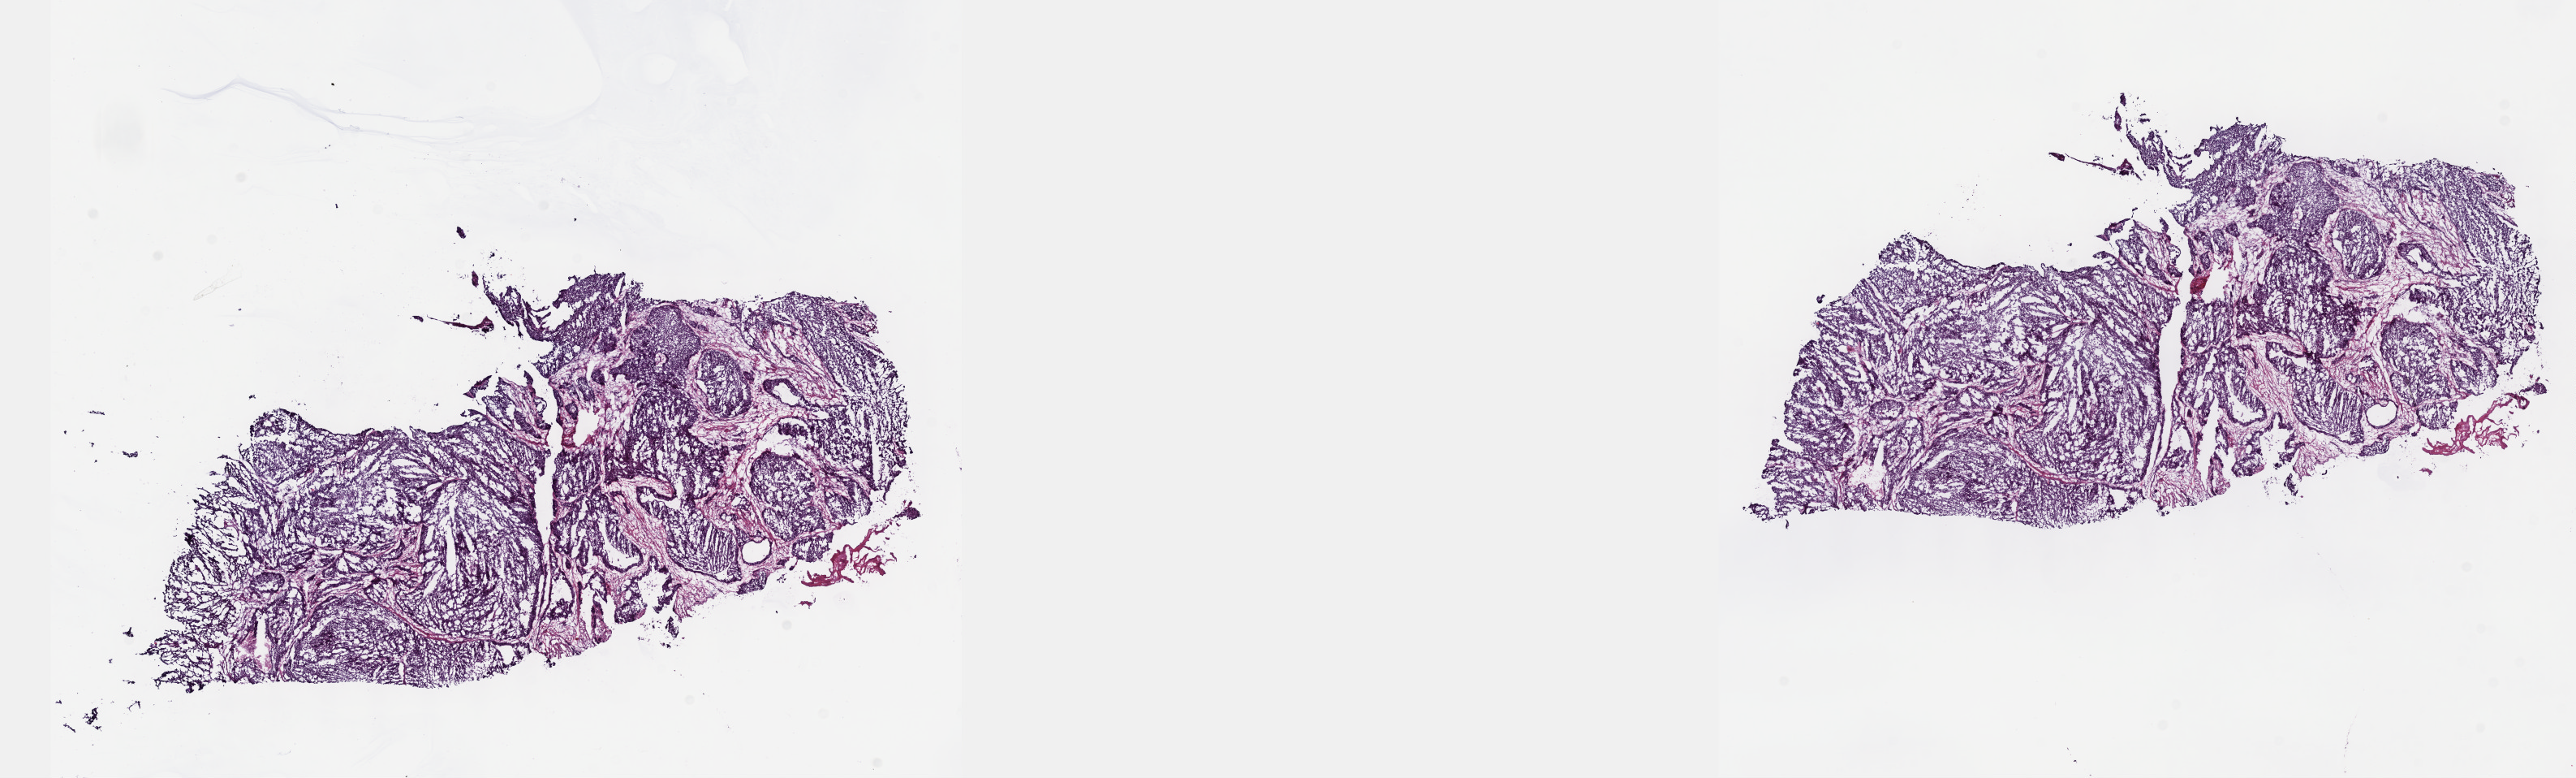
Whole-slide histology image, H&E-stained — low-resolution overview of the scanned area, about 25.7 x 7.7 mm (from a 40x scan). Frozen section from the top of the tissue portion. Sample: primary tumour, bladder. Male patient; age at initial diagnosis 46 years. Histologic grade: high grade. Composition of this section per pathologist review: tumour cells 80%, tumour nuclei 90%, normal cells 0%, stromal cells 20%, necrosis 0%. Infiltration values recorded for this section: lymphocyte infiltration 0%, monocyte infiltration 0%, neutrophil infiltration 0%.
- histologic diagnosis: Papillary transitional cell carcinoma
- AJCC pathologic stage: III (7th edition)
- TNM: T3a N0 MX
- lymph nodes positive (case pathology): 0 of 21 examined